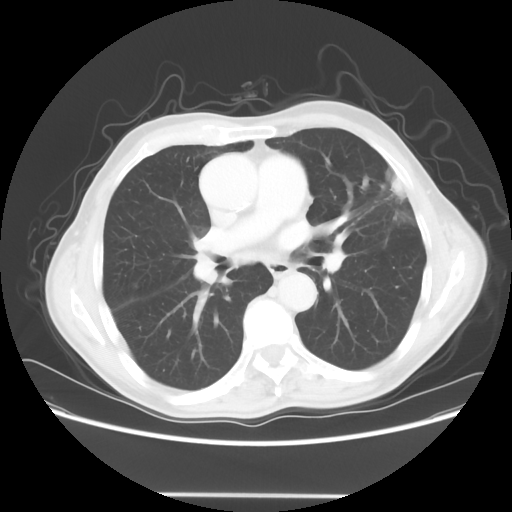
Chest CT, one axial slice. Slice 35 of 64 in the series (ordered by position). 120 kVp. Lung window (W 1500 / L -600 HU). 5 mm slice thickness. 512 × 512 image matrix. Patient: male, 71 years. Case-level facts recorded for this patient, not image findings: clinical TNM (as recorded): T1c N0 M0.
Annotated regions visible in this slice (rectangle marked by the reading radiologist):
- lung tumour (recorded histology: adenocarcinoma): bounding box [x1, y1, x2, y2] px = [381, 164, 408, 206]